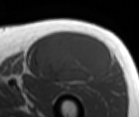
MRI of an extremity soft-tissue mass, one axial slice; slice 61 of 86 in the series (ordered by position); MR volume resampled by the dataset authors to the PET/CT grid (not the native acquisition matrix); 3.27 mm slice thickness; 139 × 117 image matrix, field of view 136 × 114 mm. Male patient. From the clinical record (not read from this slice): histological type: extraskeletal osteosarcoma; grade: high; site of the primary tumour: thigh.
Structures marked on this image (expert contour drawn on MRI and transferred to this co-registered scan by the dataset authors):
- gross tumour volume (mass): box from (x=36, y=32) to (x=112, y=83) px